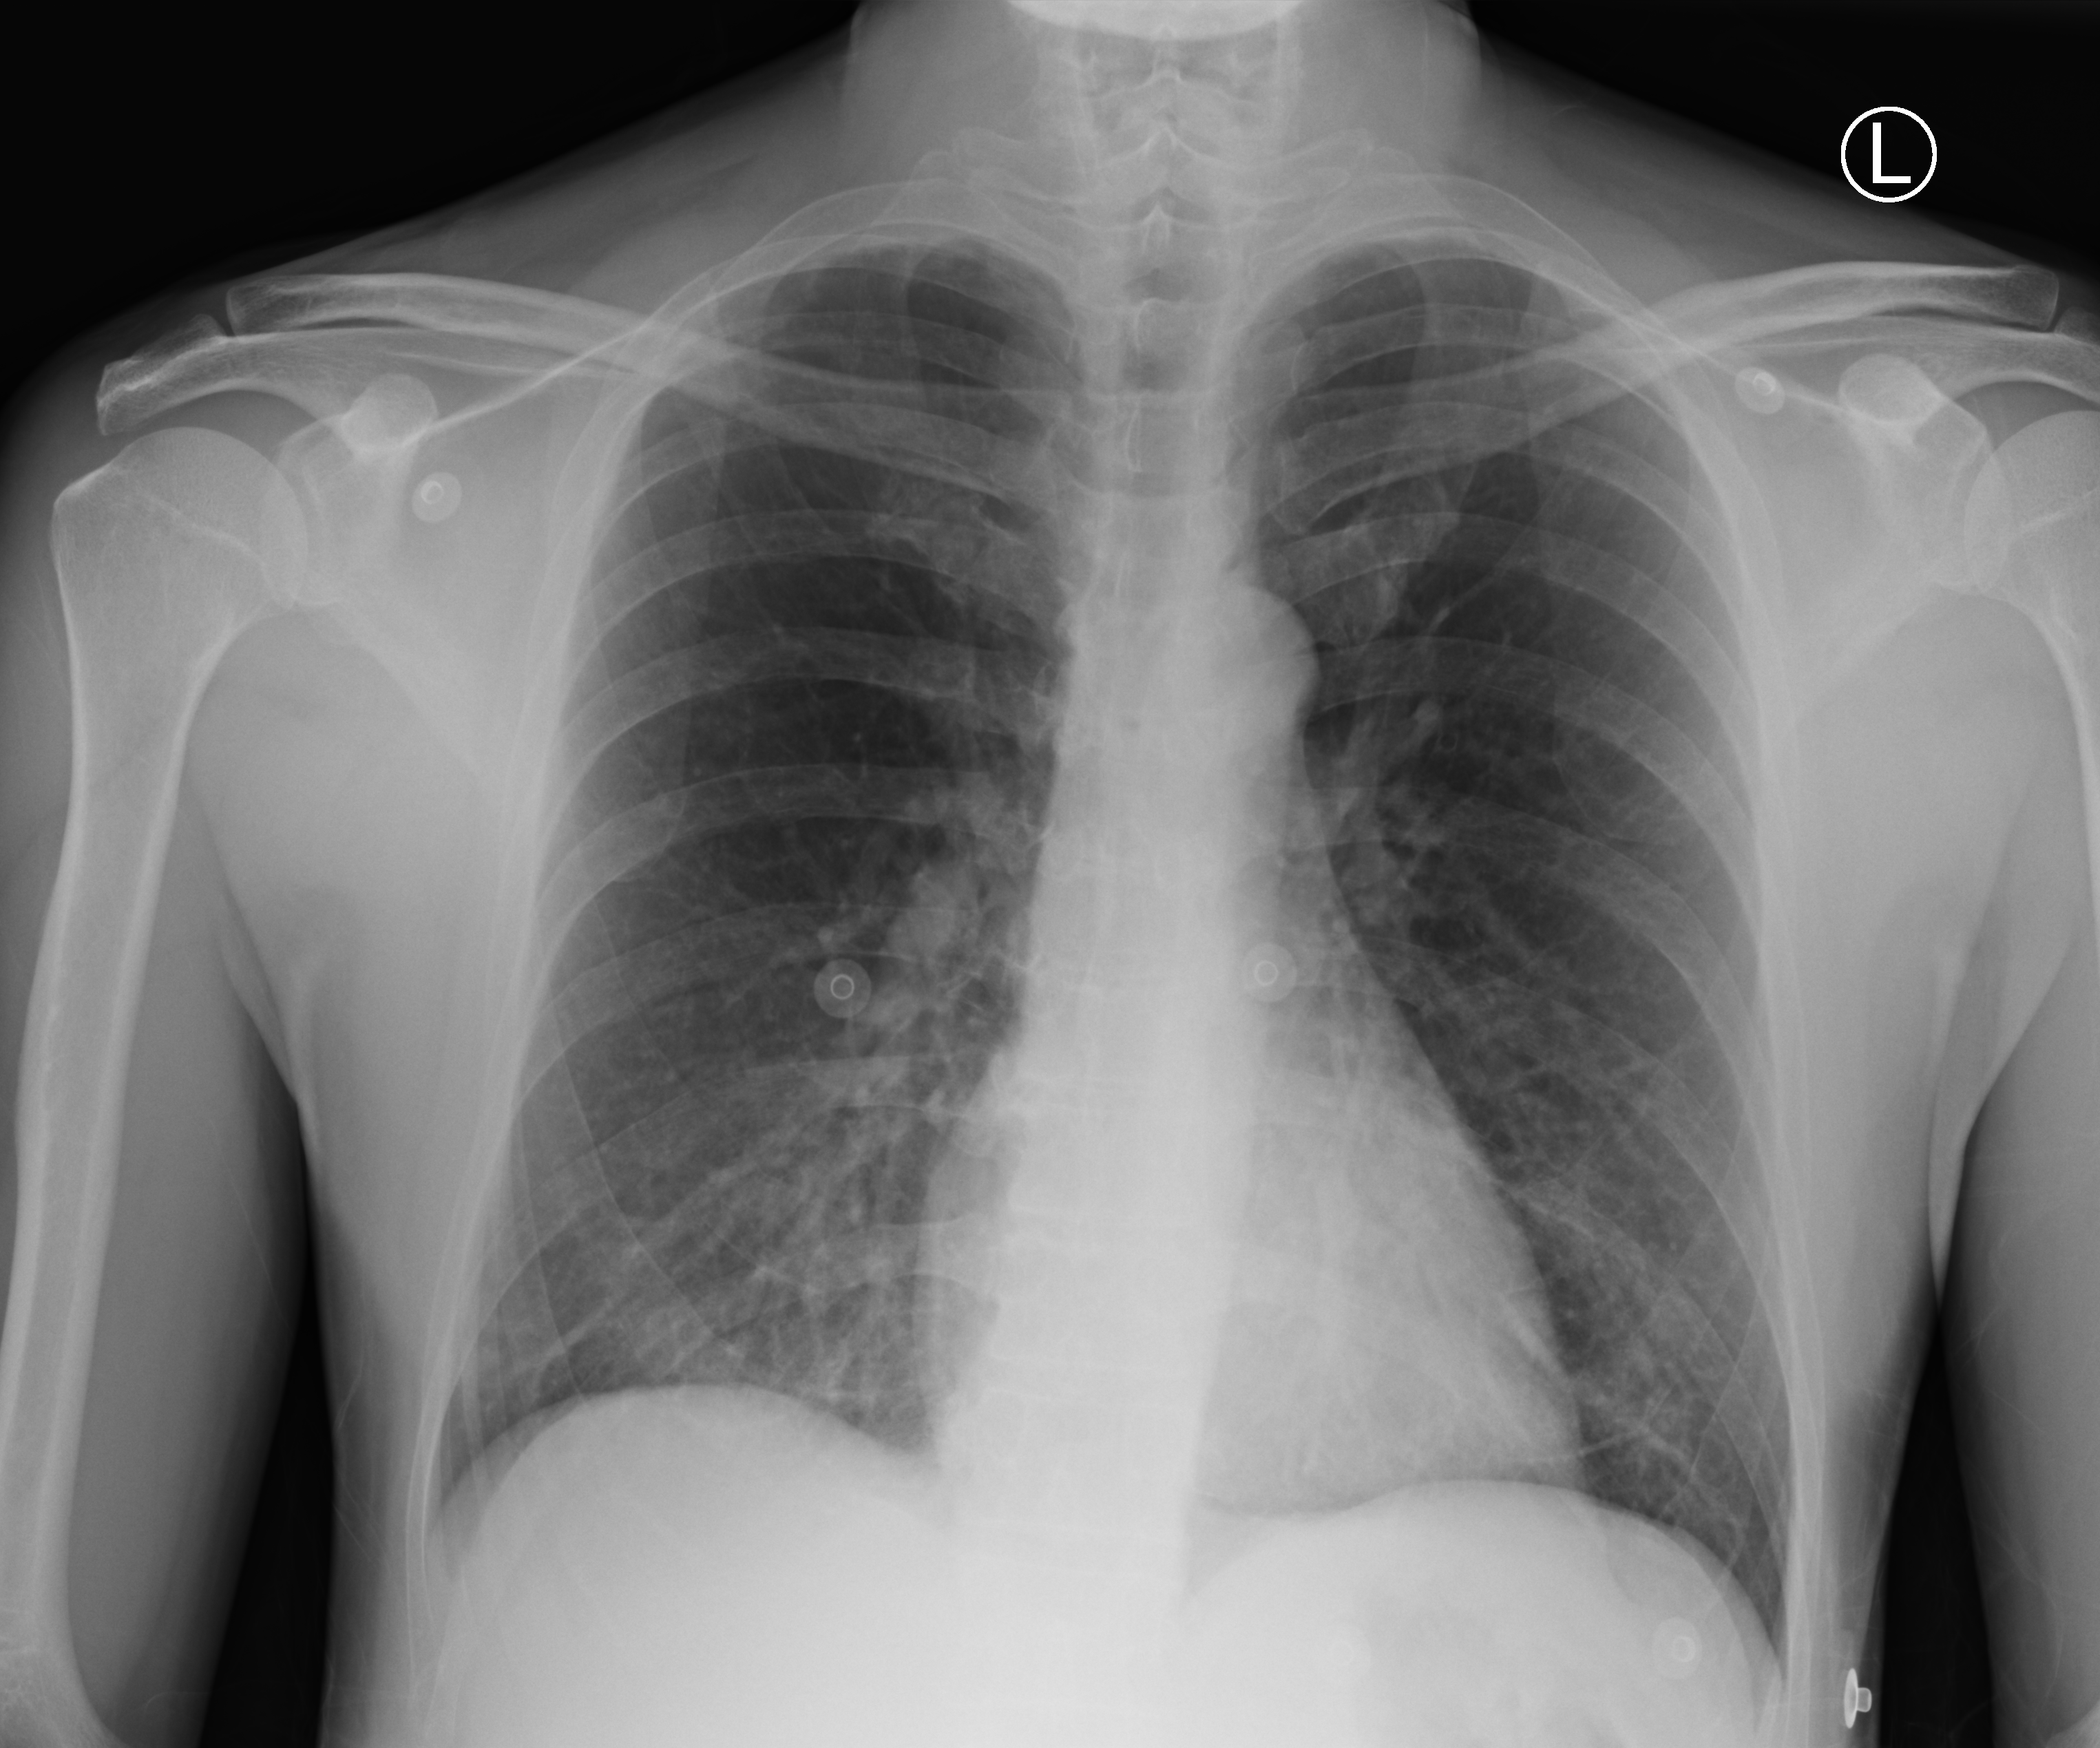
Bedside chest radiograph (computed radiography), anteroposterior (AP) projection. Male patient hospitalised with COVID-19, age 18–59 years.
Hospital-stay facts (about this admission, not read from this image; timing relative to this image not recorded): admitted to intensive care during this hospital stay: no; mechanically ventilated during this hospital stay: no.